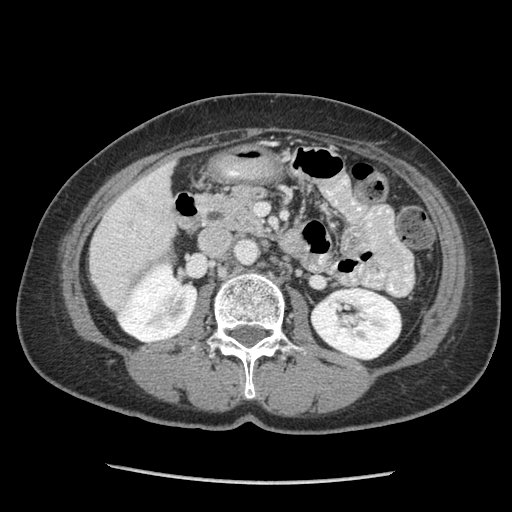
Contrast-enhanced abdominal CT (liver protocol), one axial slice. Position 27 of 105 along the scan axis. 140 kVp. Soft-tissue window (W 400 / L 40 HU). 512 × 512 image matrix, field of view 340 × 340 mm. Case-level facts recorded for this patient, not image findings: diagnosis: hepatocellular carcinoma (patient treated with transarterial chemoembolisation; whether this scan precedes or follows treatment is not stated here); TNM stage (as recorded): Stage-I; Child-Pugh class: A; tumour nodularity: uninodular; tumour size: 11.1 cm.
Structures marked on this image (semi-automatically segmented with operator editing):
- liver parenchyma outside the tumour (the mass and vessels are separate outlines, so this box may not span the whole liver): box from (x=90, y=160) to (x=176, y=308) px
- liver vessels: (x=113, y=178)–(x=151, y=238)